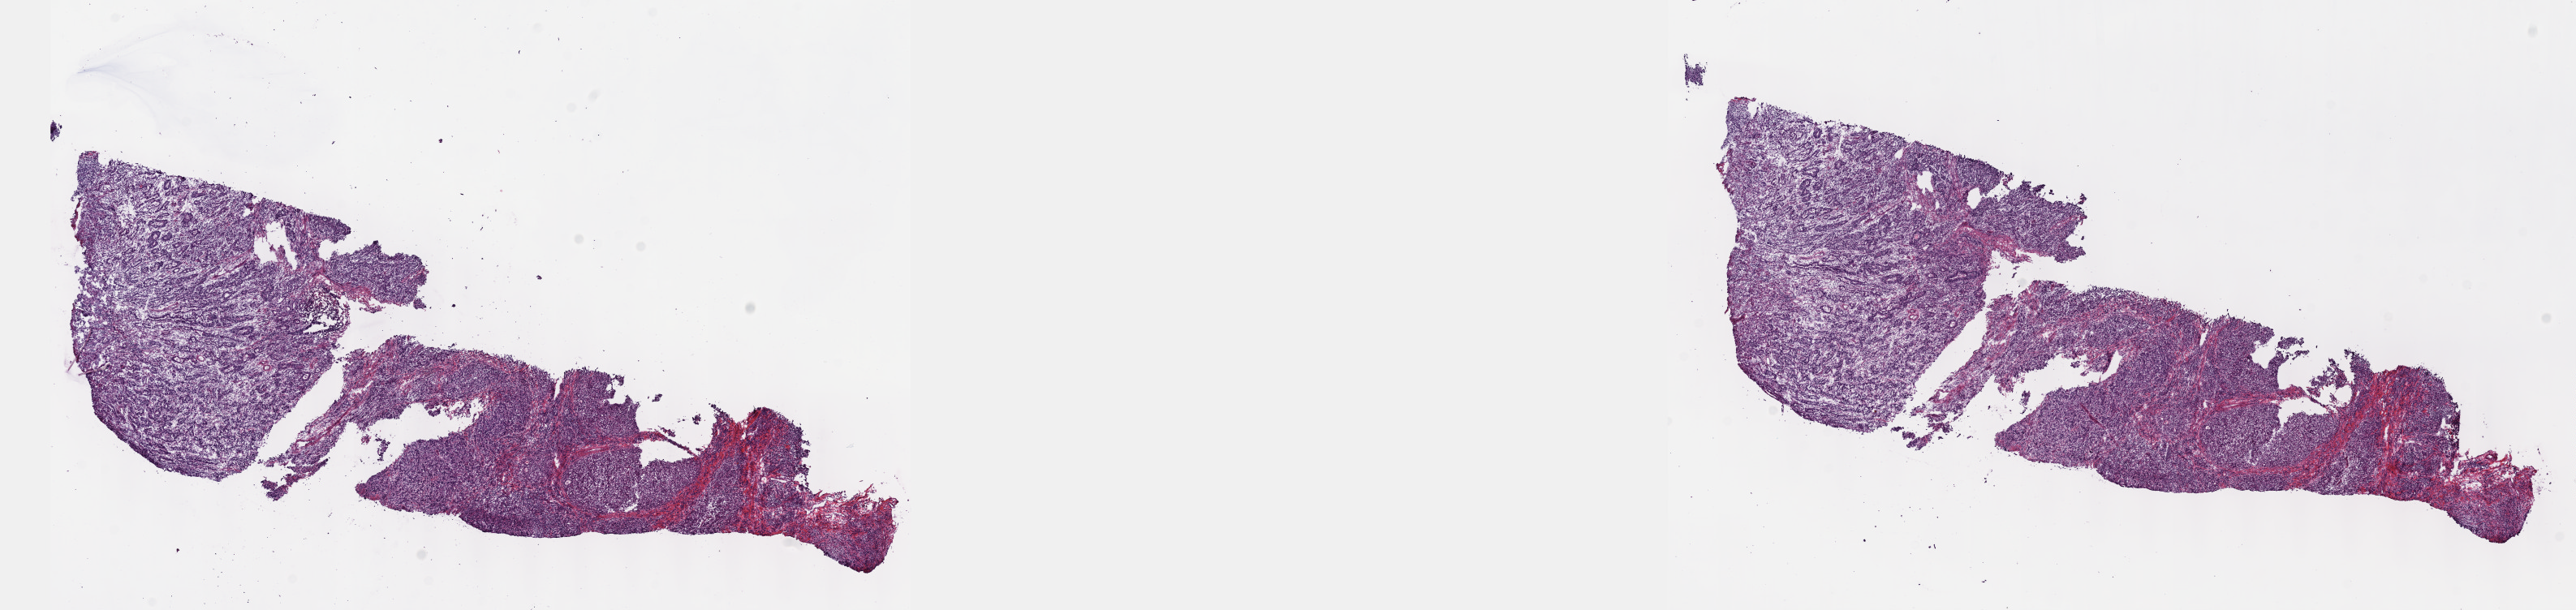
Whole-slide histology image, H&E — shown as a low-resolution overview of the whole scanned area (about 25.7 x 6.1 mm). Frozen section from the top of the tissue portion. Sample: primary tumour, stomach. Patient: male, age at initial diagnosis 76 years. Histologic grade: G3 (poorly differentiated). Pathologist review of this section (percent, as recorded): tumour cells 75%, tumour nuclei 75%, normal cells 0%, stromal cells 25%, necrosis 0%. Inflammatory infiltration, as recorded: lymphocyte infiltration 2%, monocyte infiltration 1%, neutrophil infiltration 4%.
Histologic diagnosis: Tubular adenocarcinoma (body of stomach). AJCC pathologic stage: IIIB (7th edition).